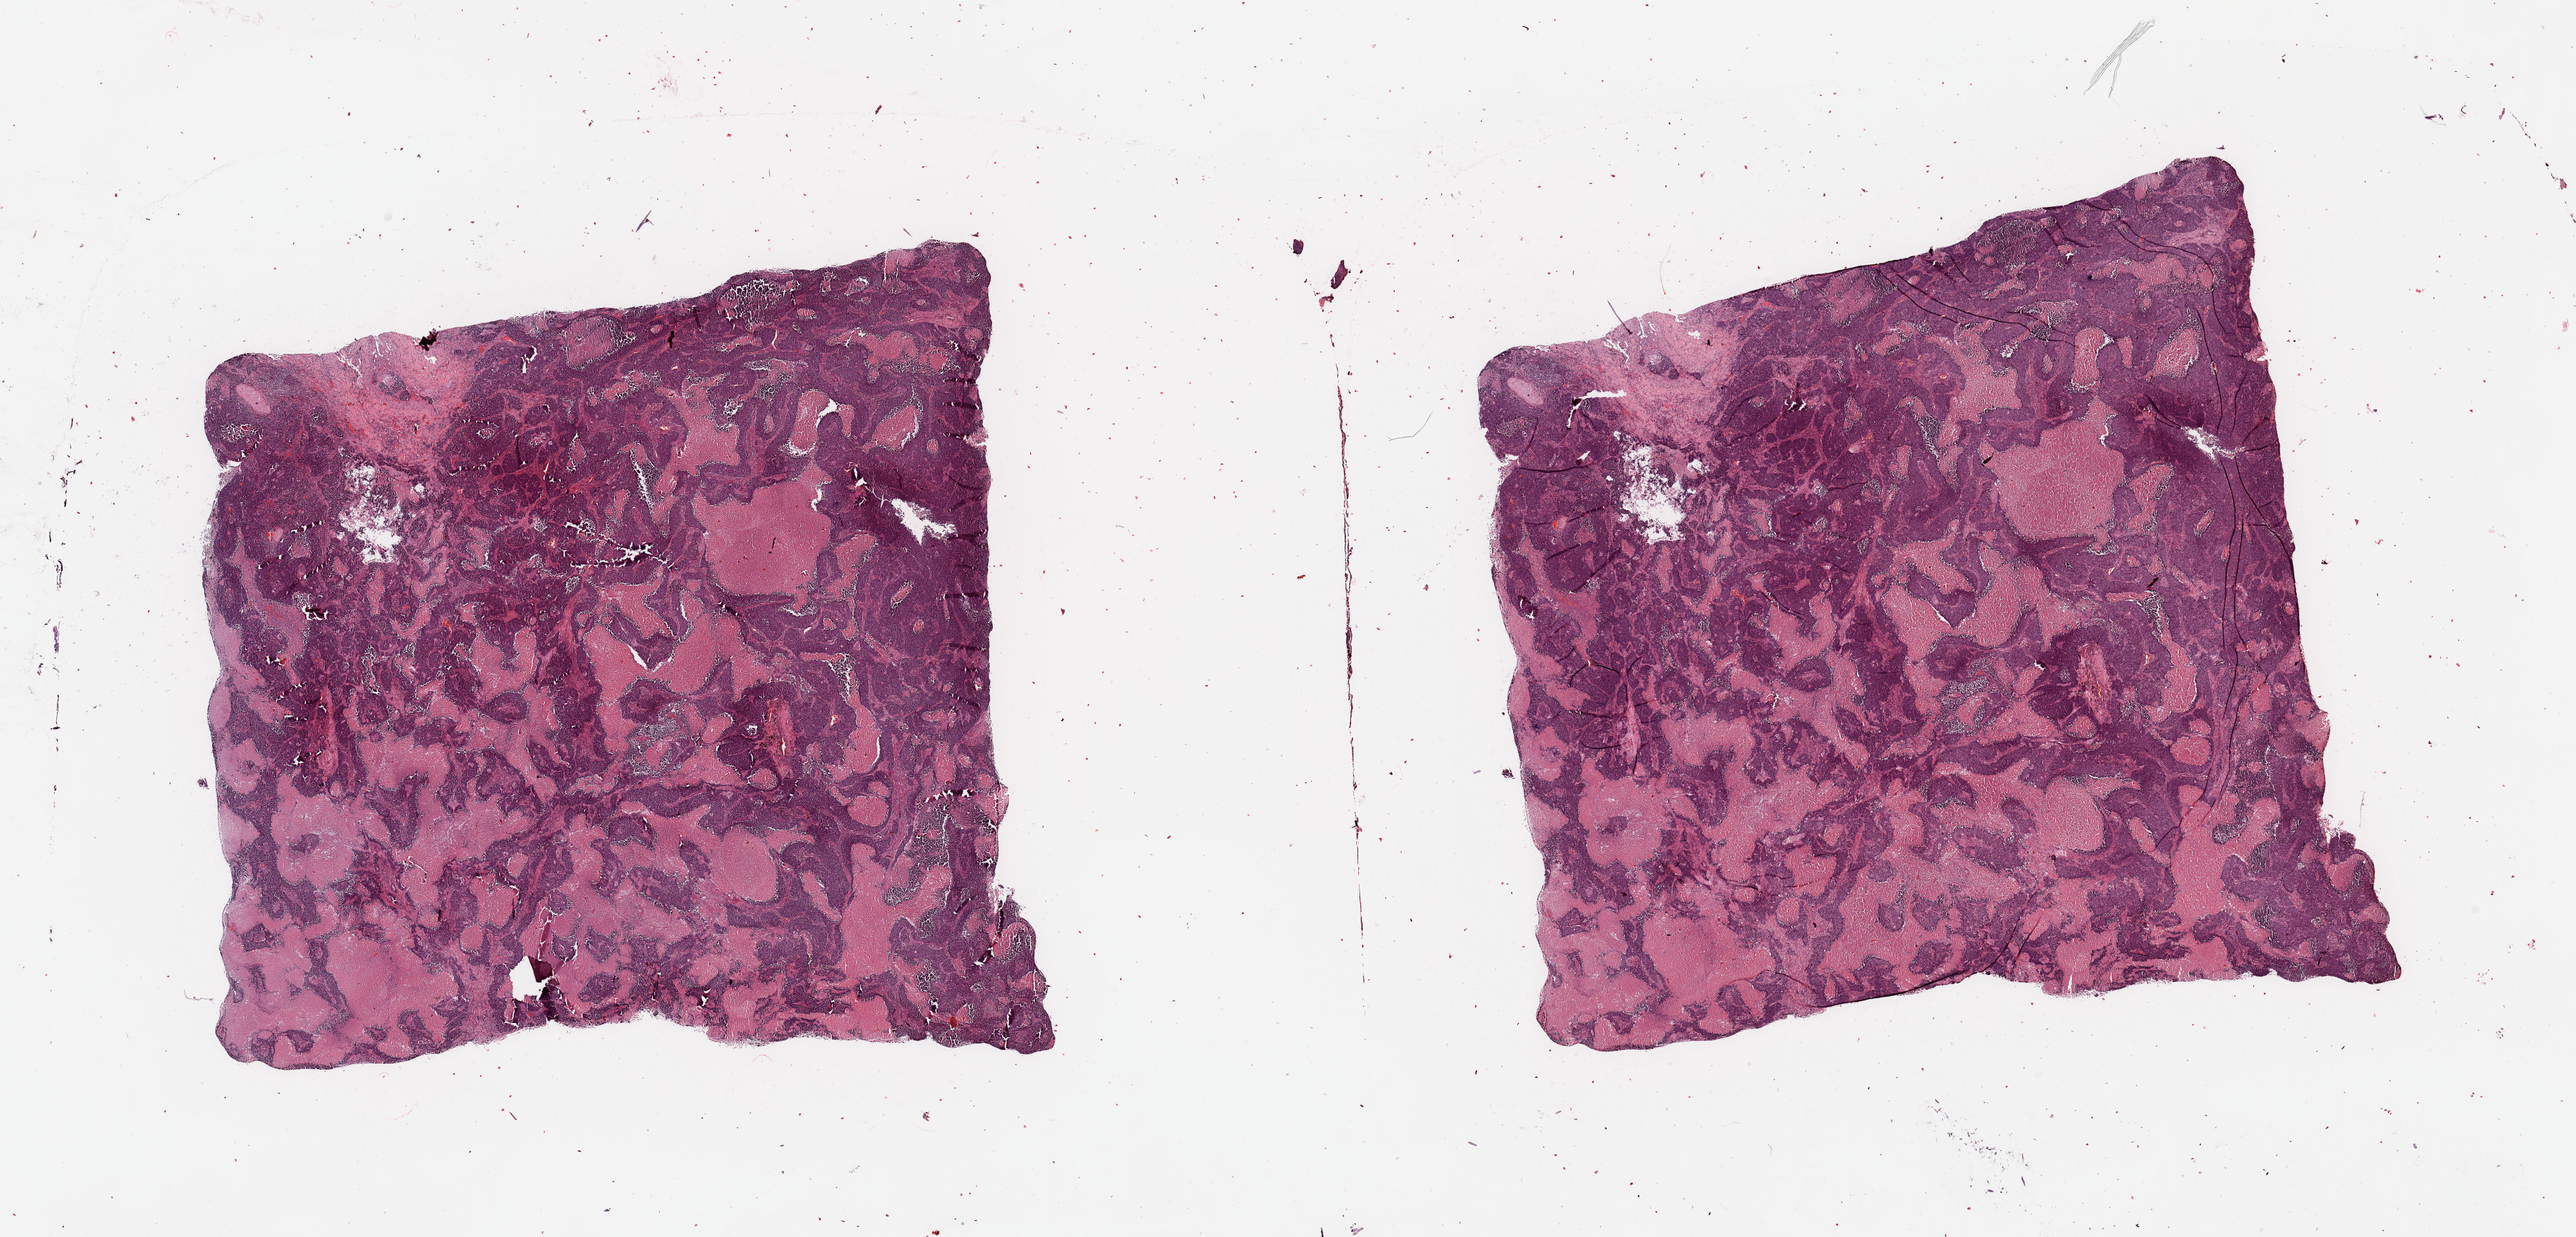
Digitized Hematoxylin and eosin (H&E) stained tissue section (whole slide) — shown as a low-resolution overview of the whole scanned area (about 31.5 x 15.1 mm, slide scanned at 20x); lung, tumour tissue. 61-year-old male patient.
Histologic diagnosis: Squamous cell carcinoma, NOS.